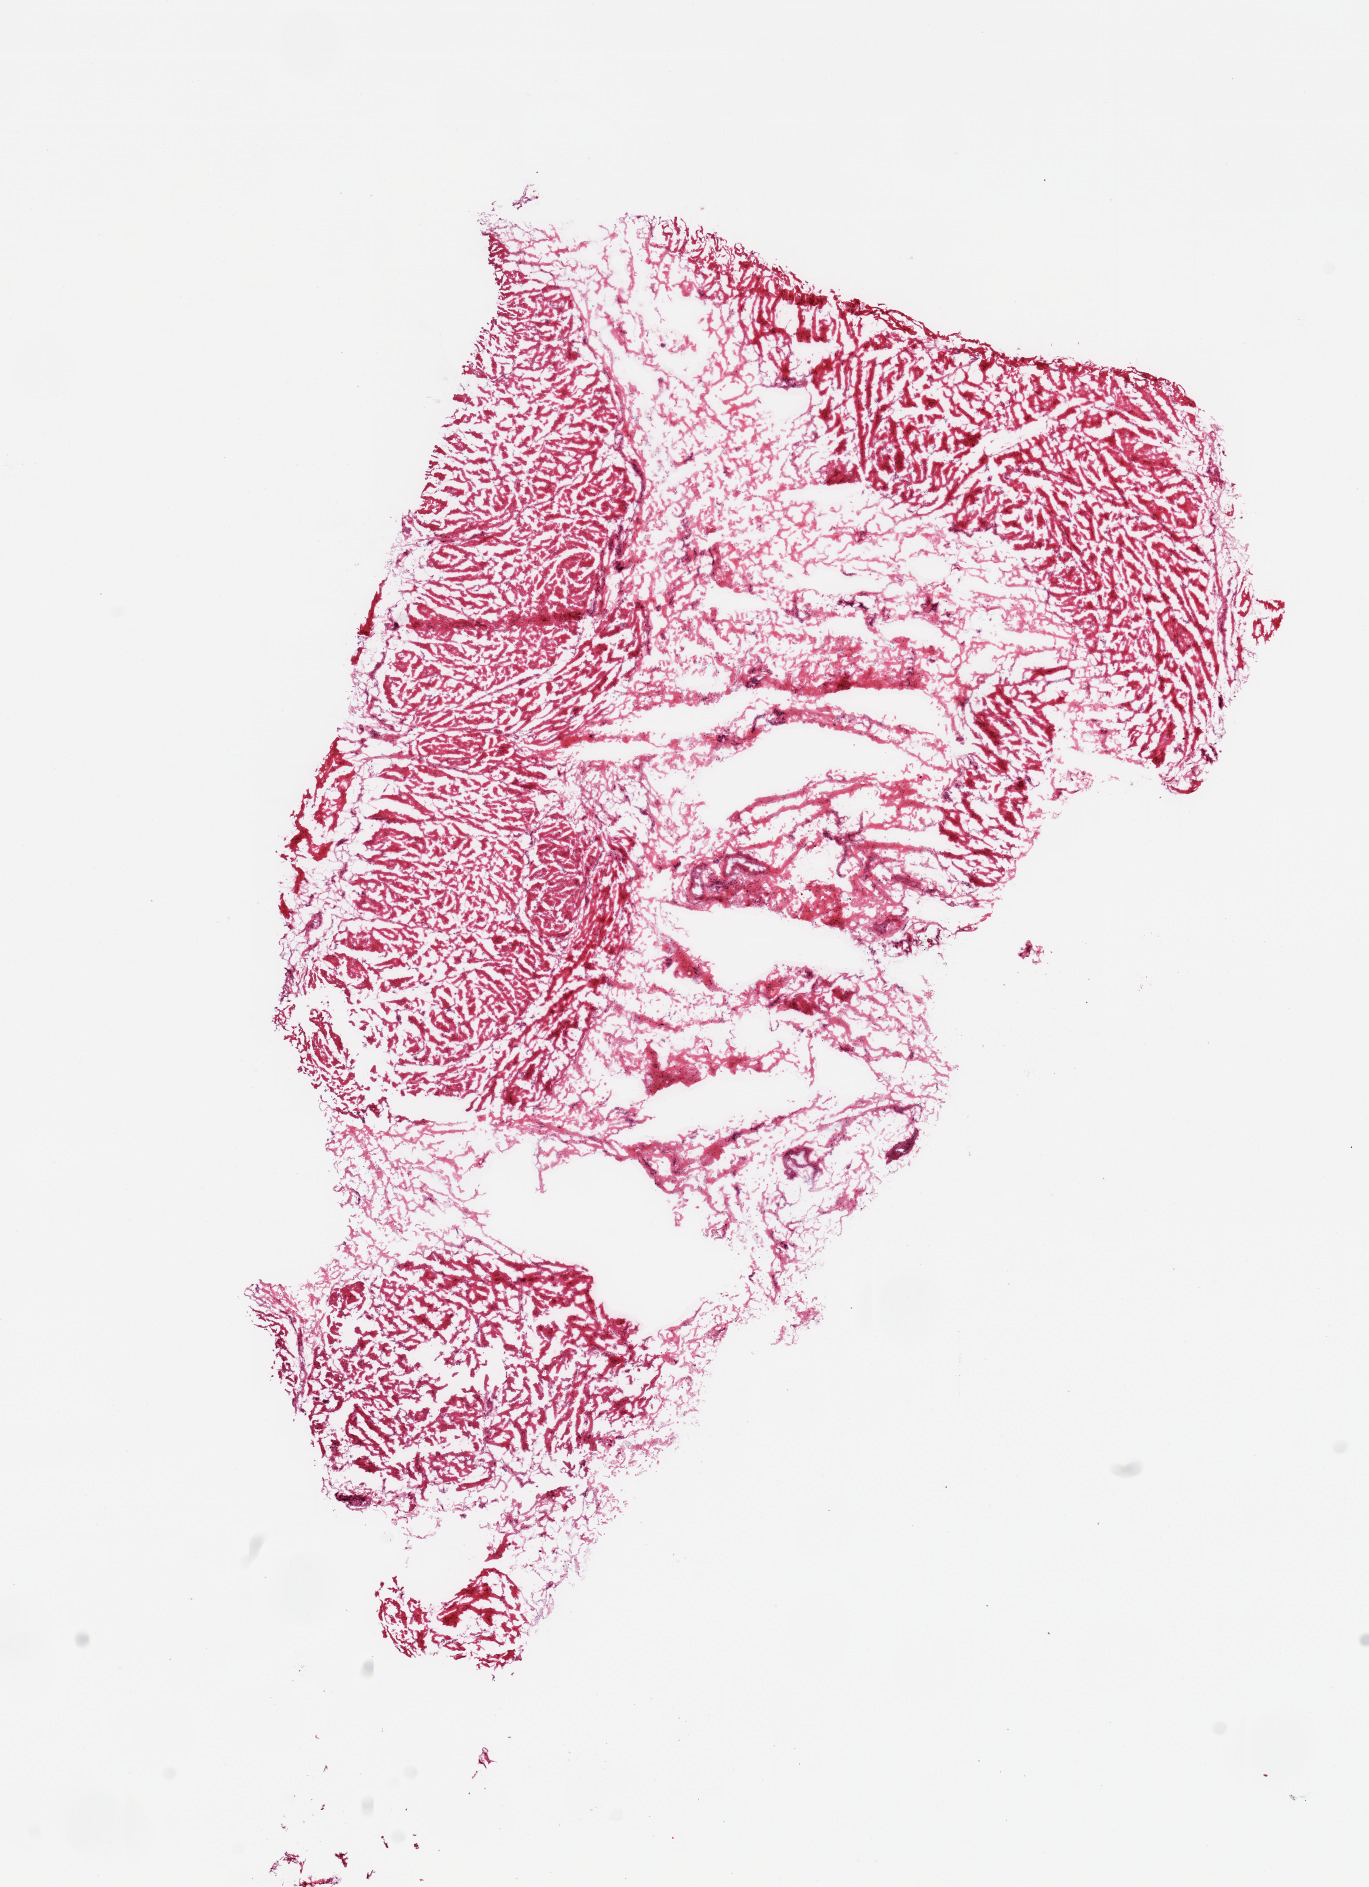
Digitized haematoxylin and eosin-stained section, brightfield — low-resolution overview of the scanned area, about 10.8 x 14.9 mm.
Specimen: frozen section; sampled site (target tissue): esophageal muscle; tissue donor sample.